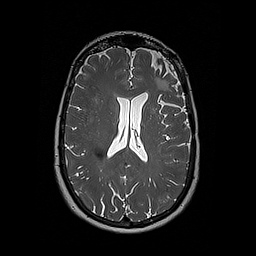
Brain MRI from a brain-tumour surgery series, one axial slice. Position 110 of 192 along the scan axis. 1 mm slice thickness. 256 × 256 image matrix. From the clinical record (not read from this slice): histopathology: Oligodendroglioma; WHO grade: 2; IDH mutation: yes; tumour location: Left Frontal.
Outlined on this slice (expert manual segmentation):
- tumour: box from (x=155, y=77) to (x=161, y=88) px